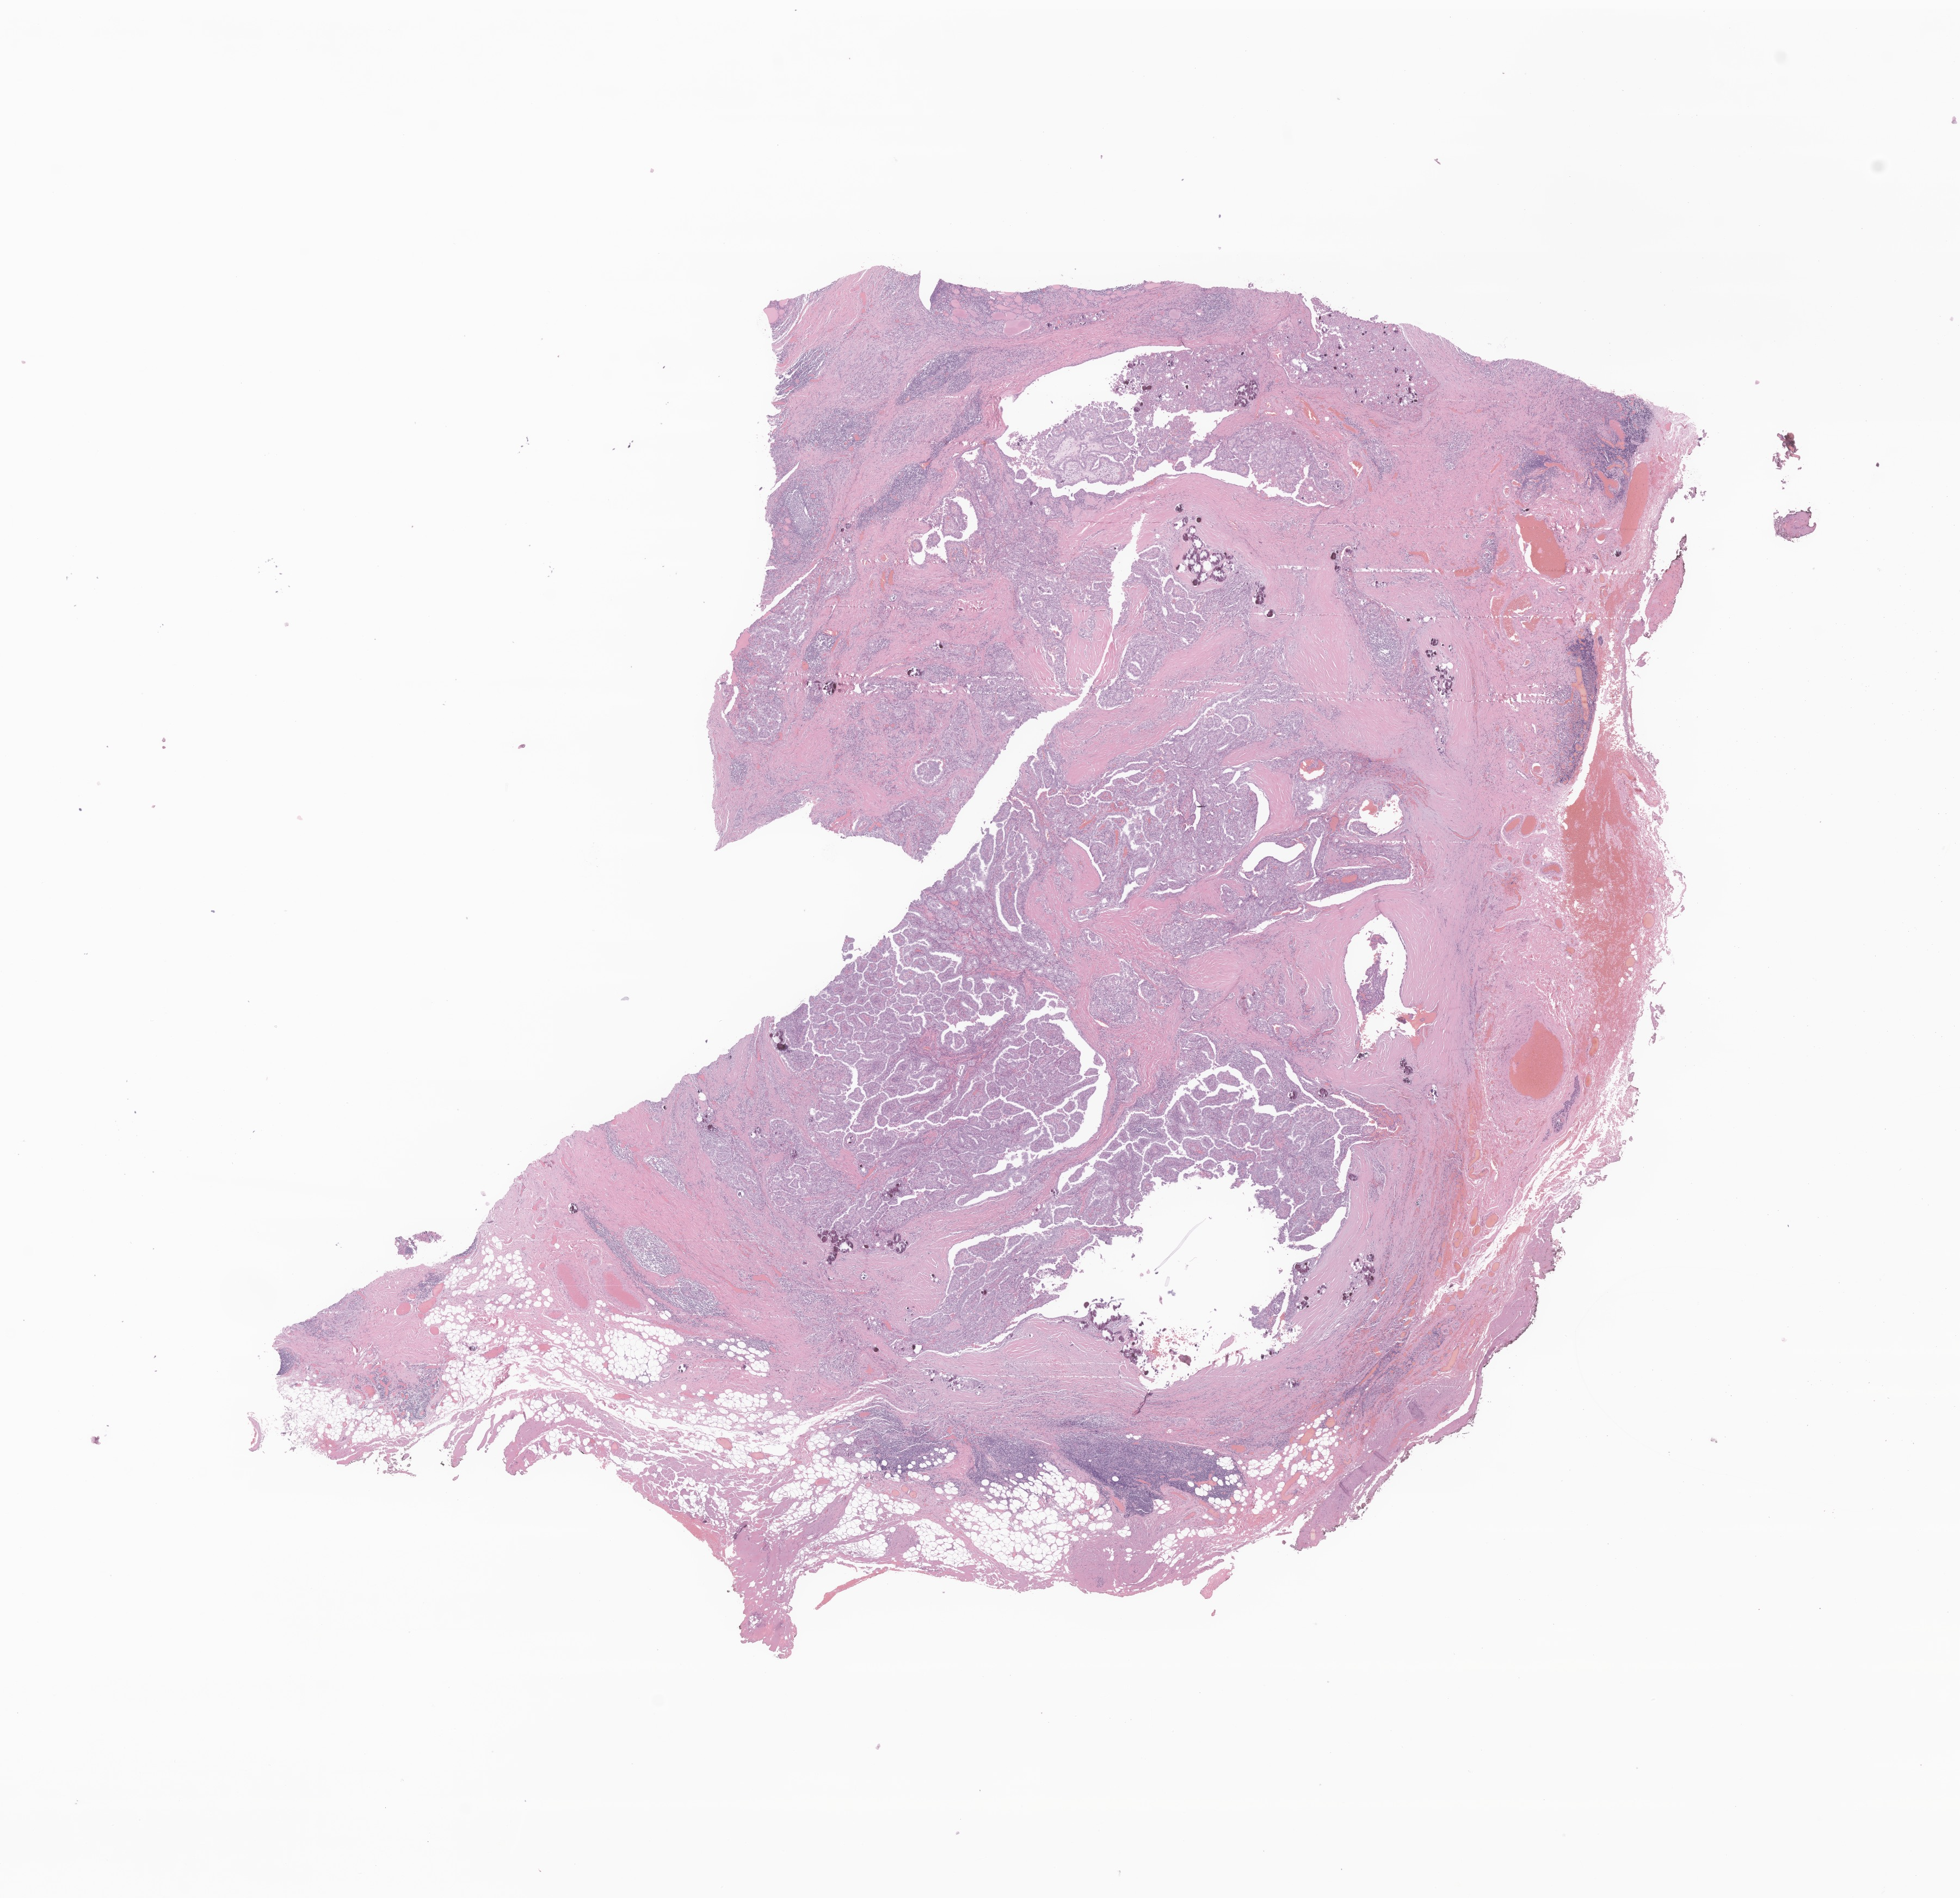
Digitized hematoxylin and eosin (H&E)-stained section of tumor tissue from the thyroid — low-resolution overview of the scanned area, about 15.2 x 14.7 mm; FFPE section. Patient: female, age 196 months.
• diagnosis: Carcinoma, metastatic, NOS